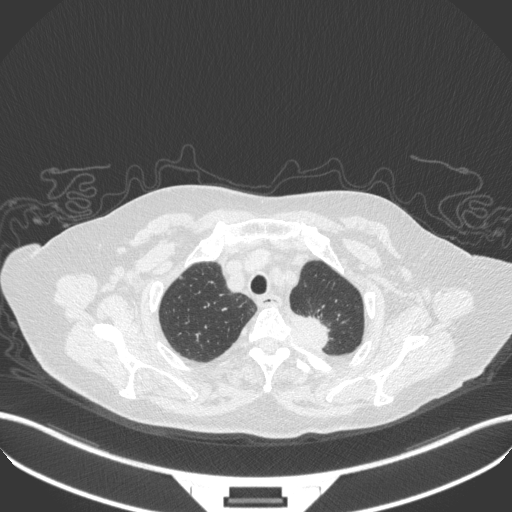
Chest CT, one axial slice; position 295 of 353 along the scan axis; lung window (W 1500 / L -600 HU); 1 mm slice thickness; 512 × 512 image matrix, field of view 400 × 400 mm. Patient: female, 81 years. Case-level facts recorded for this patient, not image findings: clinical TNM (as recorded): T2a N0 M0.
Structures marked on this image (bounding box drawn by a radiologist):
- lung tumour (recorded histology: adenocarcinoma): bounding box [x1, y1, x2, y2] px = [282, 312, 333, 348]